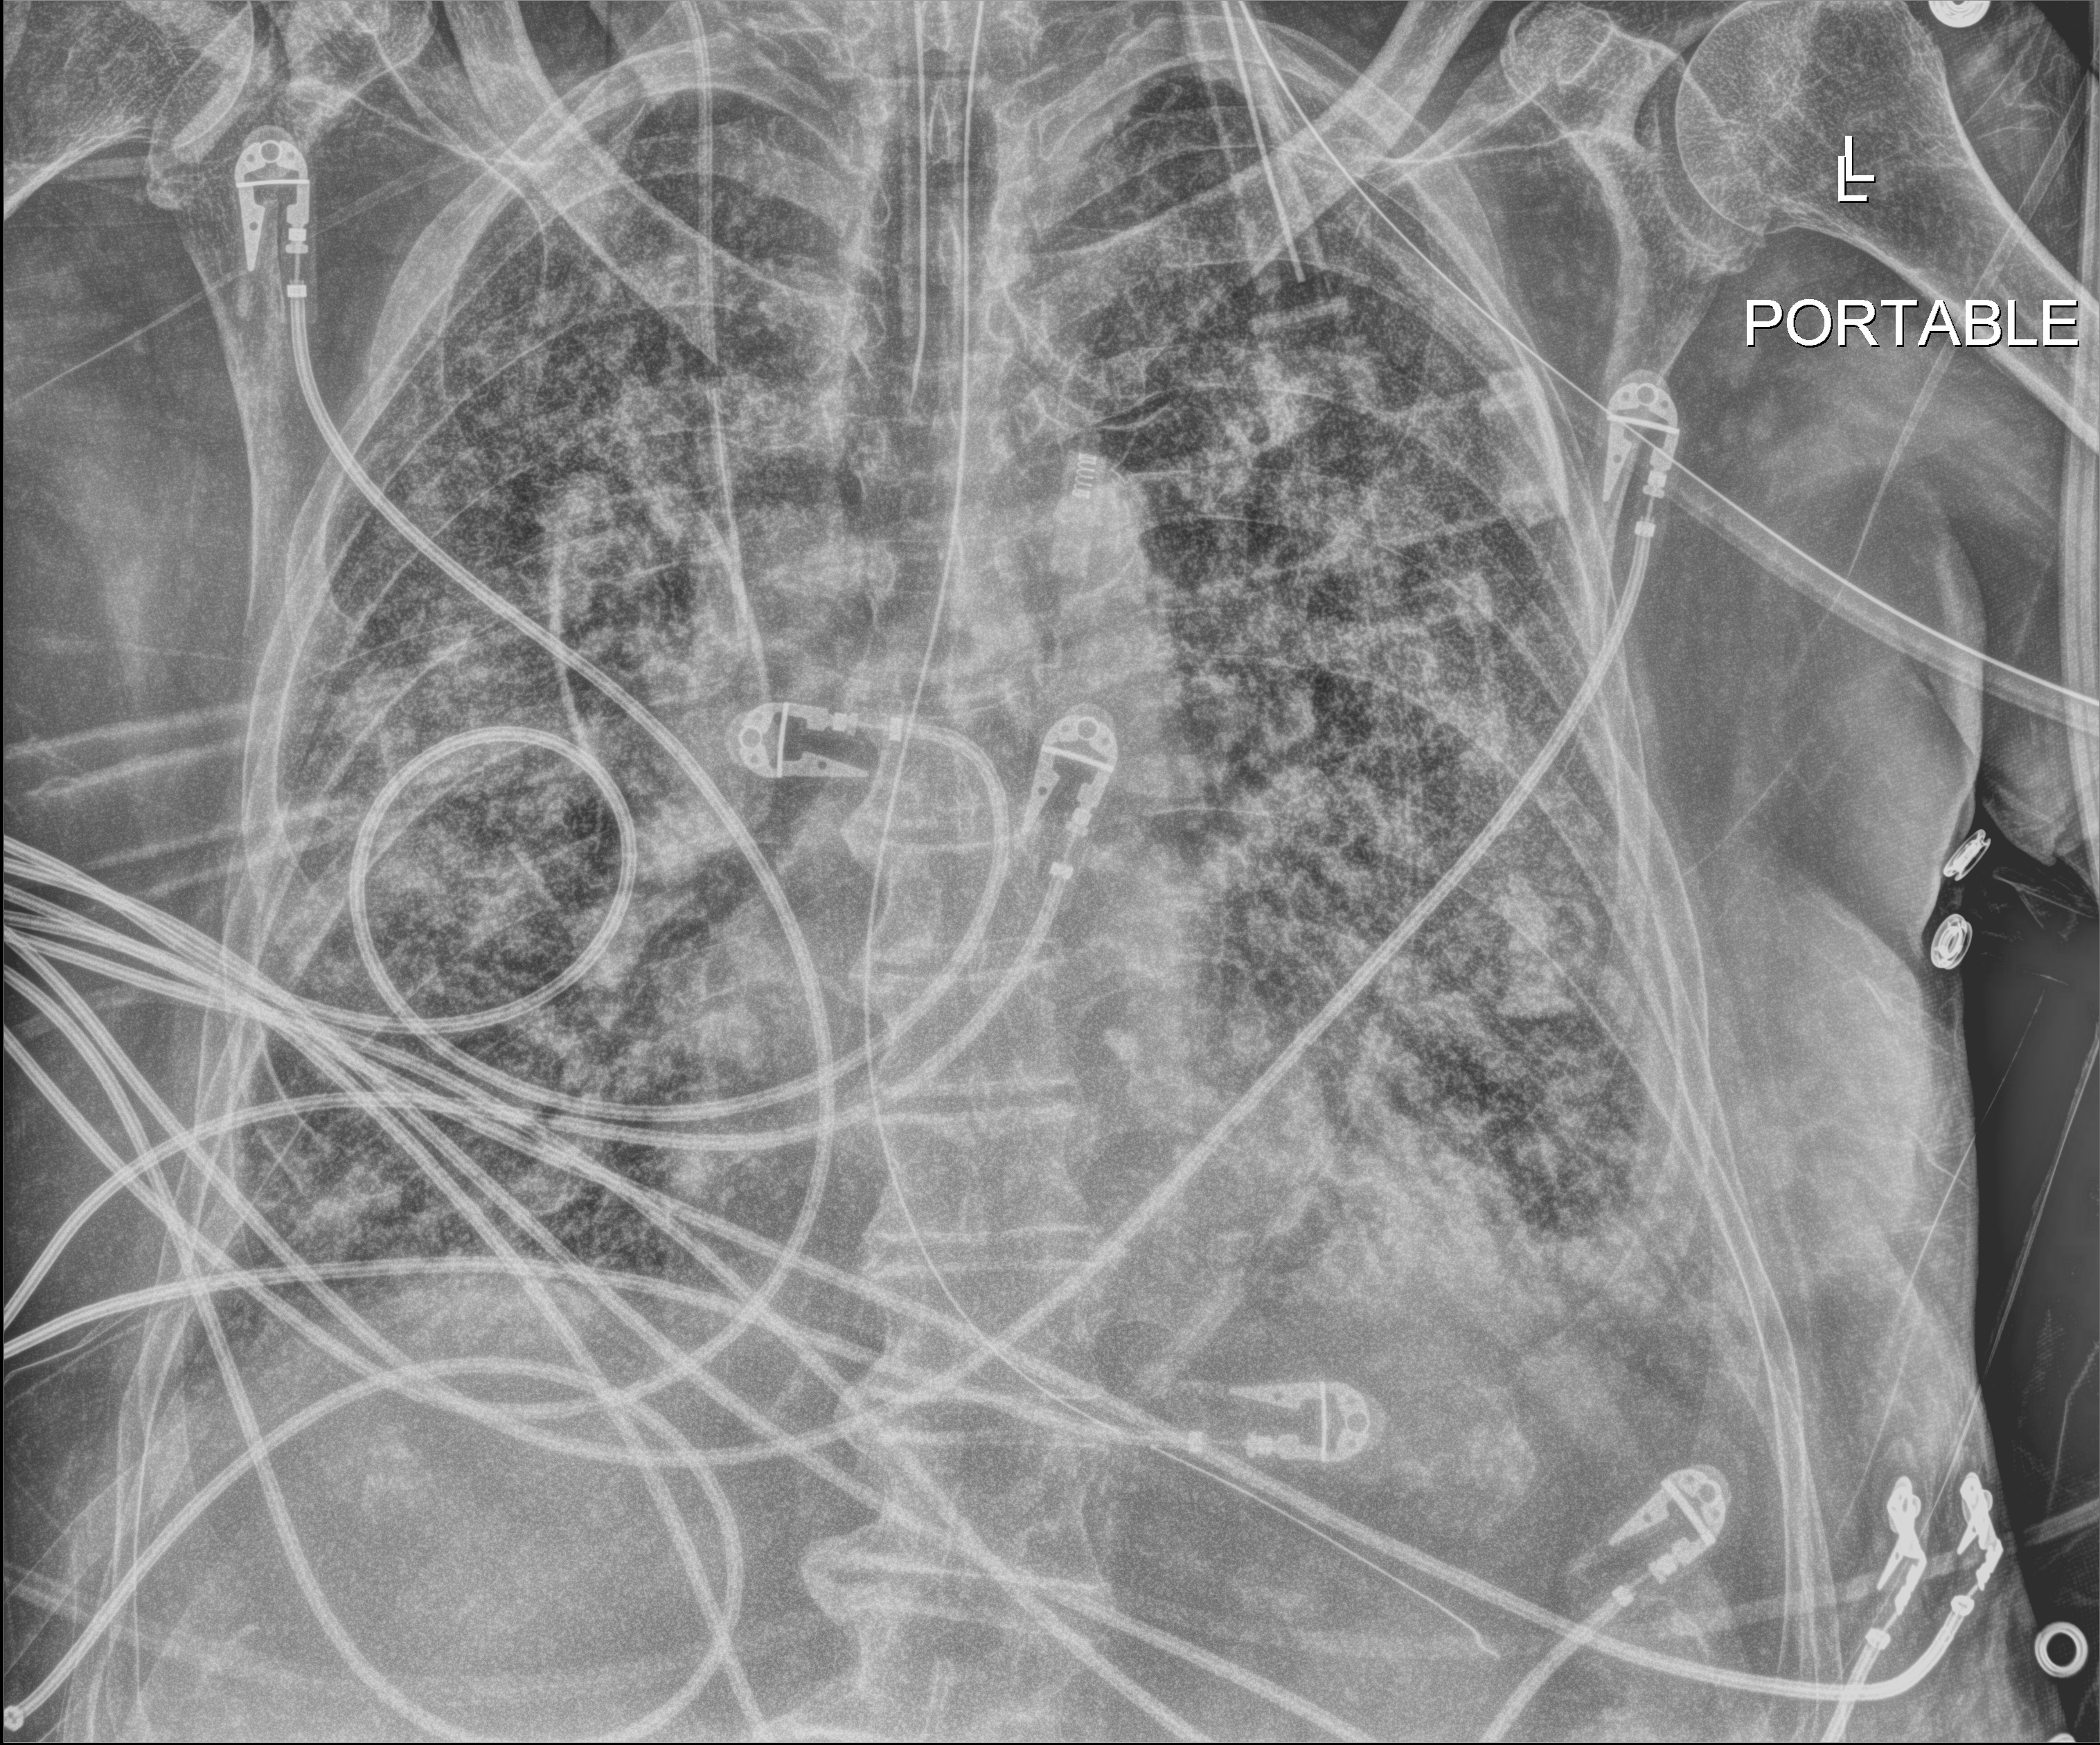
Chest X-ray (portable). Male patient hospitalised with COVID-19, age 75–90 years.
Hospital-stay facts (about this admission, not read from this image; timing relative to this image not recorded):
- hypertension (admission record): no